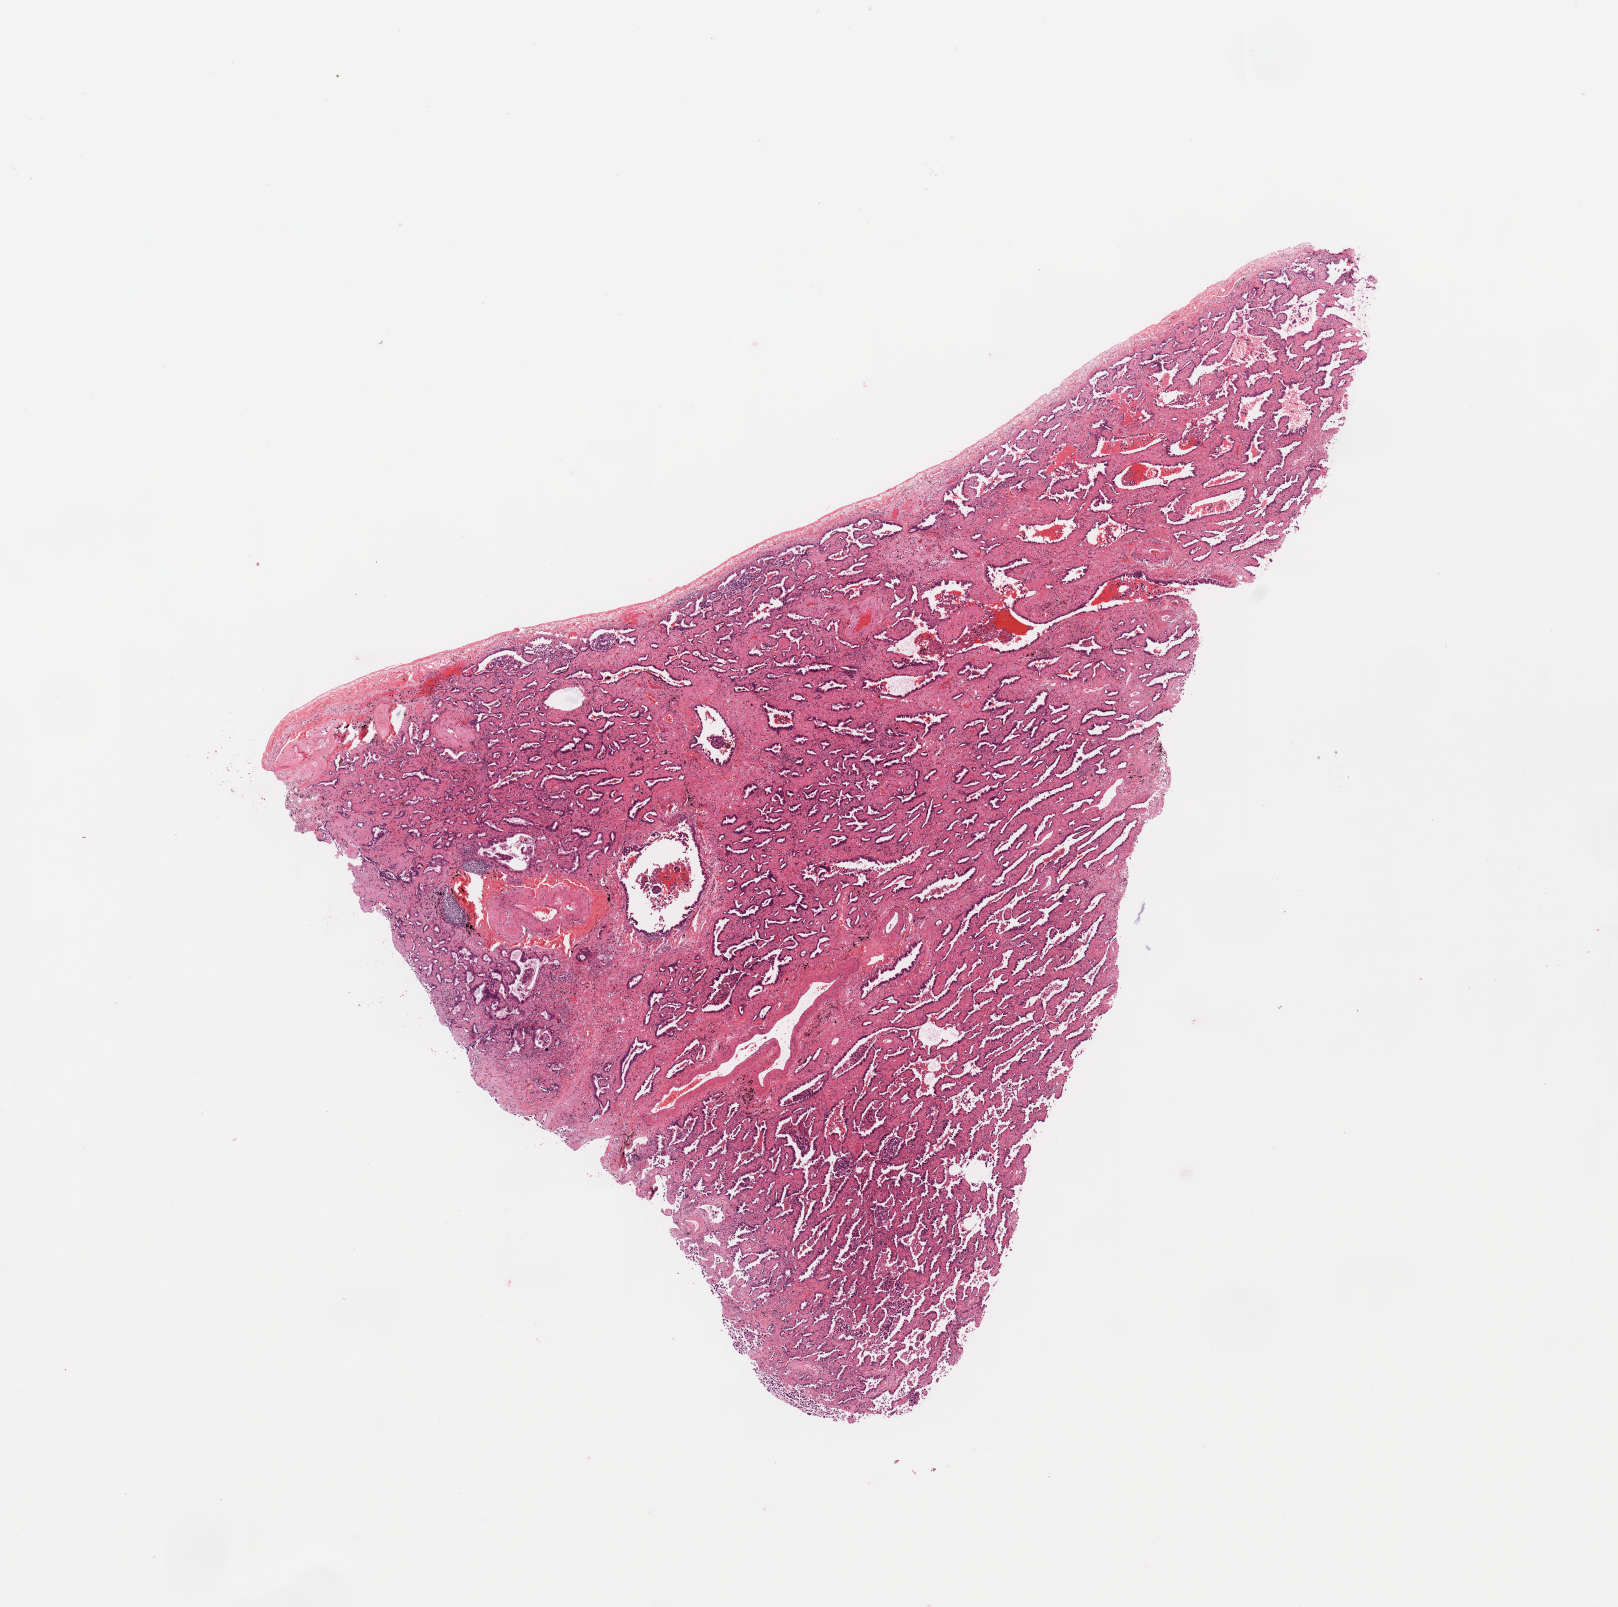
Digitized Hematoxylin and eosin (H&E) stained tissue section (whole slide) — low-resolution overview of the scanned area, about 12.8 x 12.7 mm (acquisition: 20x scan). Tumour tissue sample, sampled site: lung. Male, 76 y/o. Histologic grade: G2 (moderately differentiated). Slide review estimates, as recorded: tumour nuclei 65%, necrosis 5%.
Primary tumour site (as recorded): right upper lobe. Histologic diagnosis: Adenocarcinoma, NOS. AJCC pathologic stage: IA.